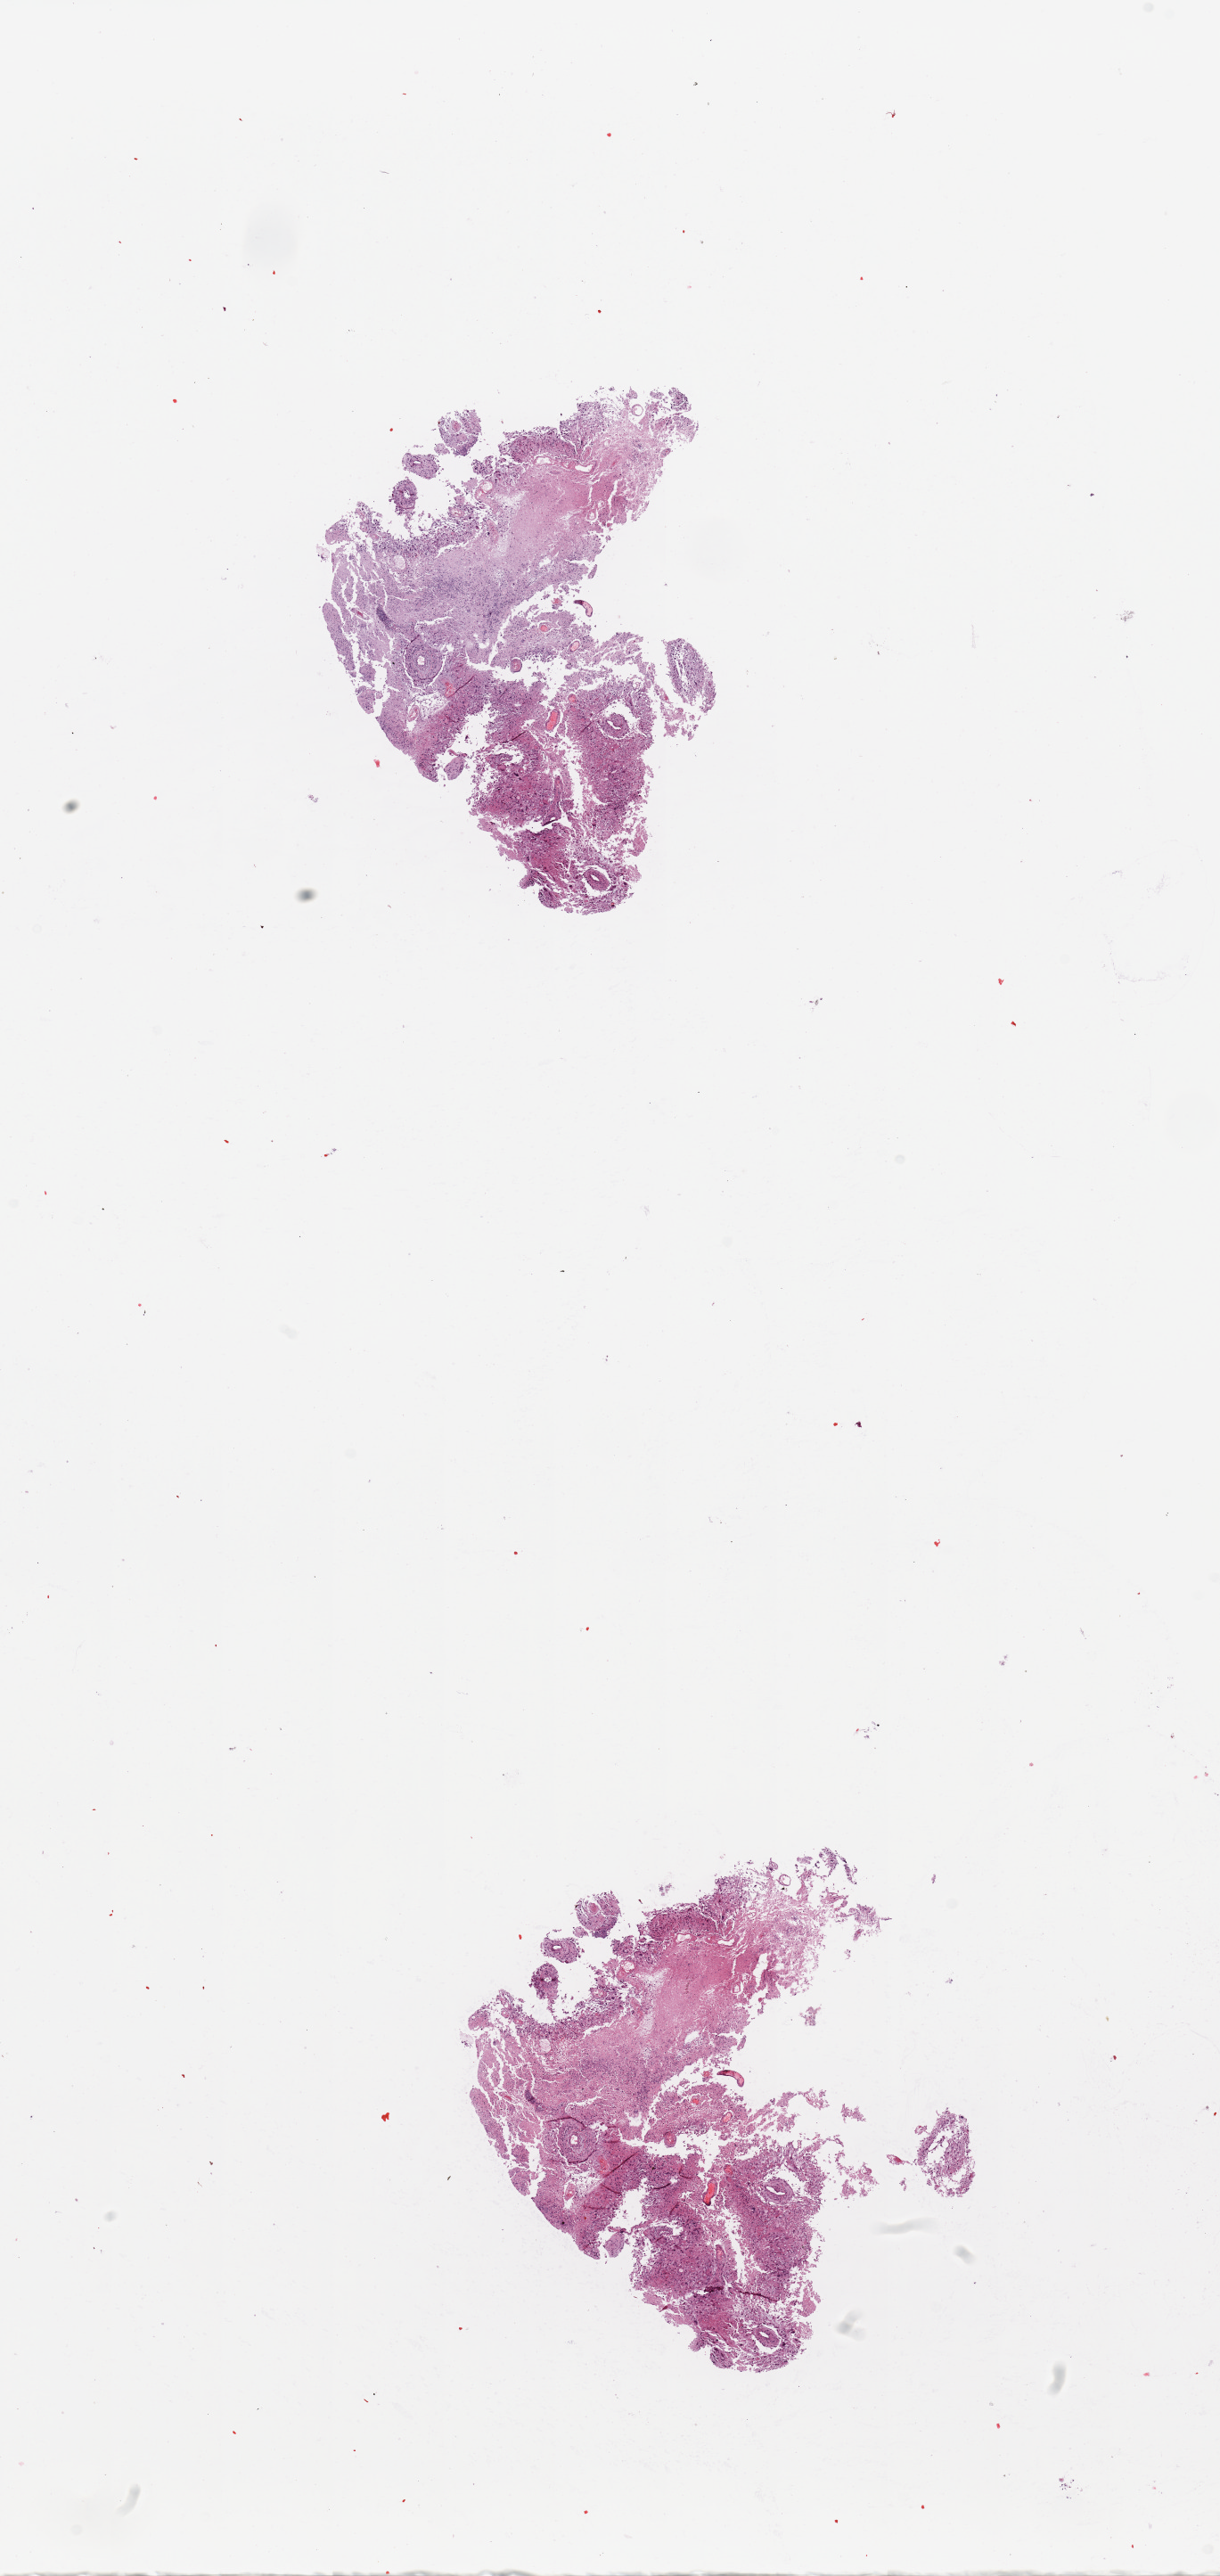
Digitized Hematoxylin and eosin (H&E) stained tissue section (whole slide), a low-resolution overview of the entire scanned area, about 10.8 x 22.9 mm, brain, tumour tissue. 37-year-old male patient.
Histologic diagnosis: Glioblastoma.